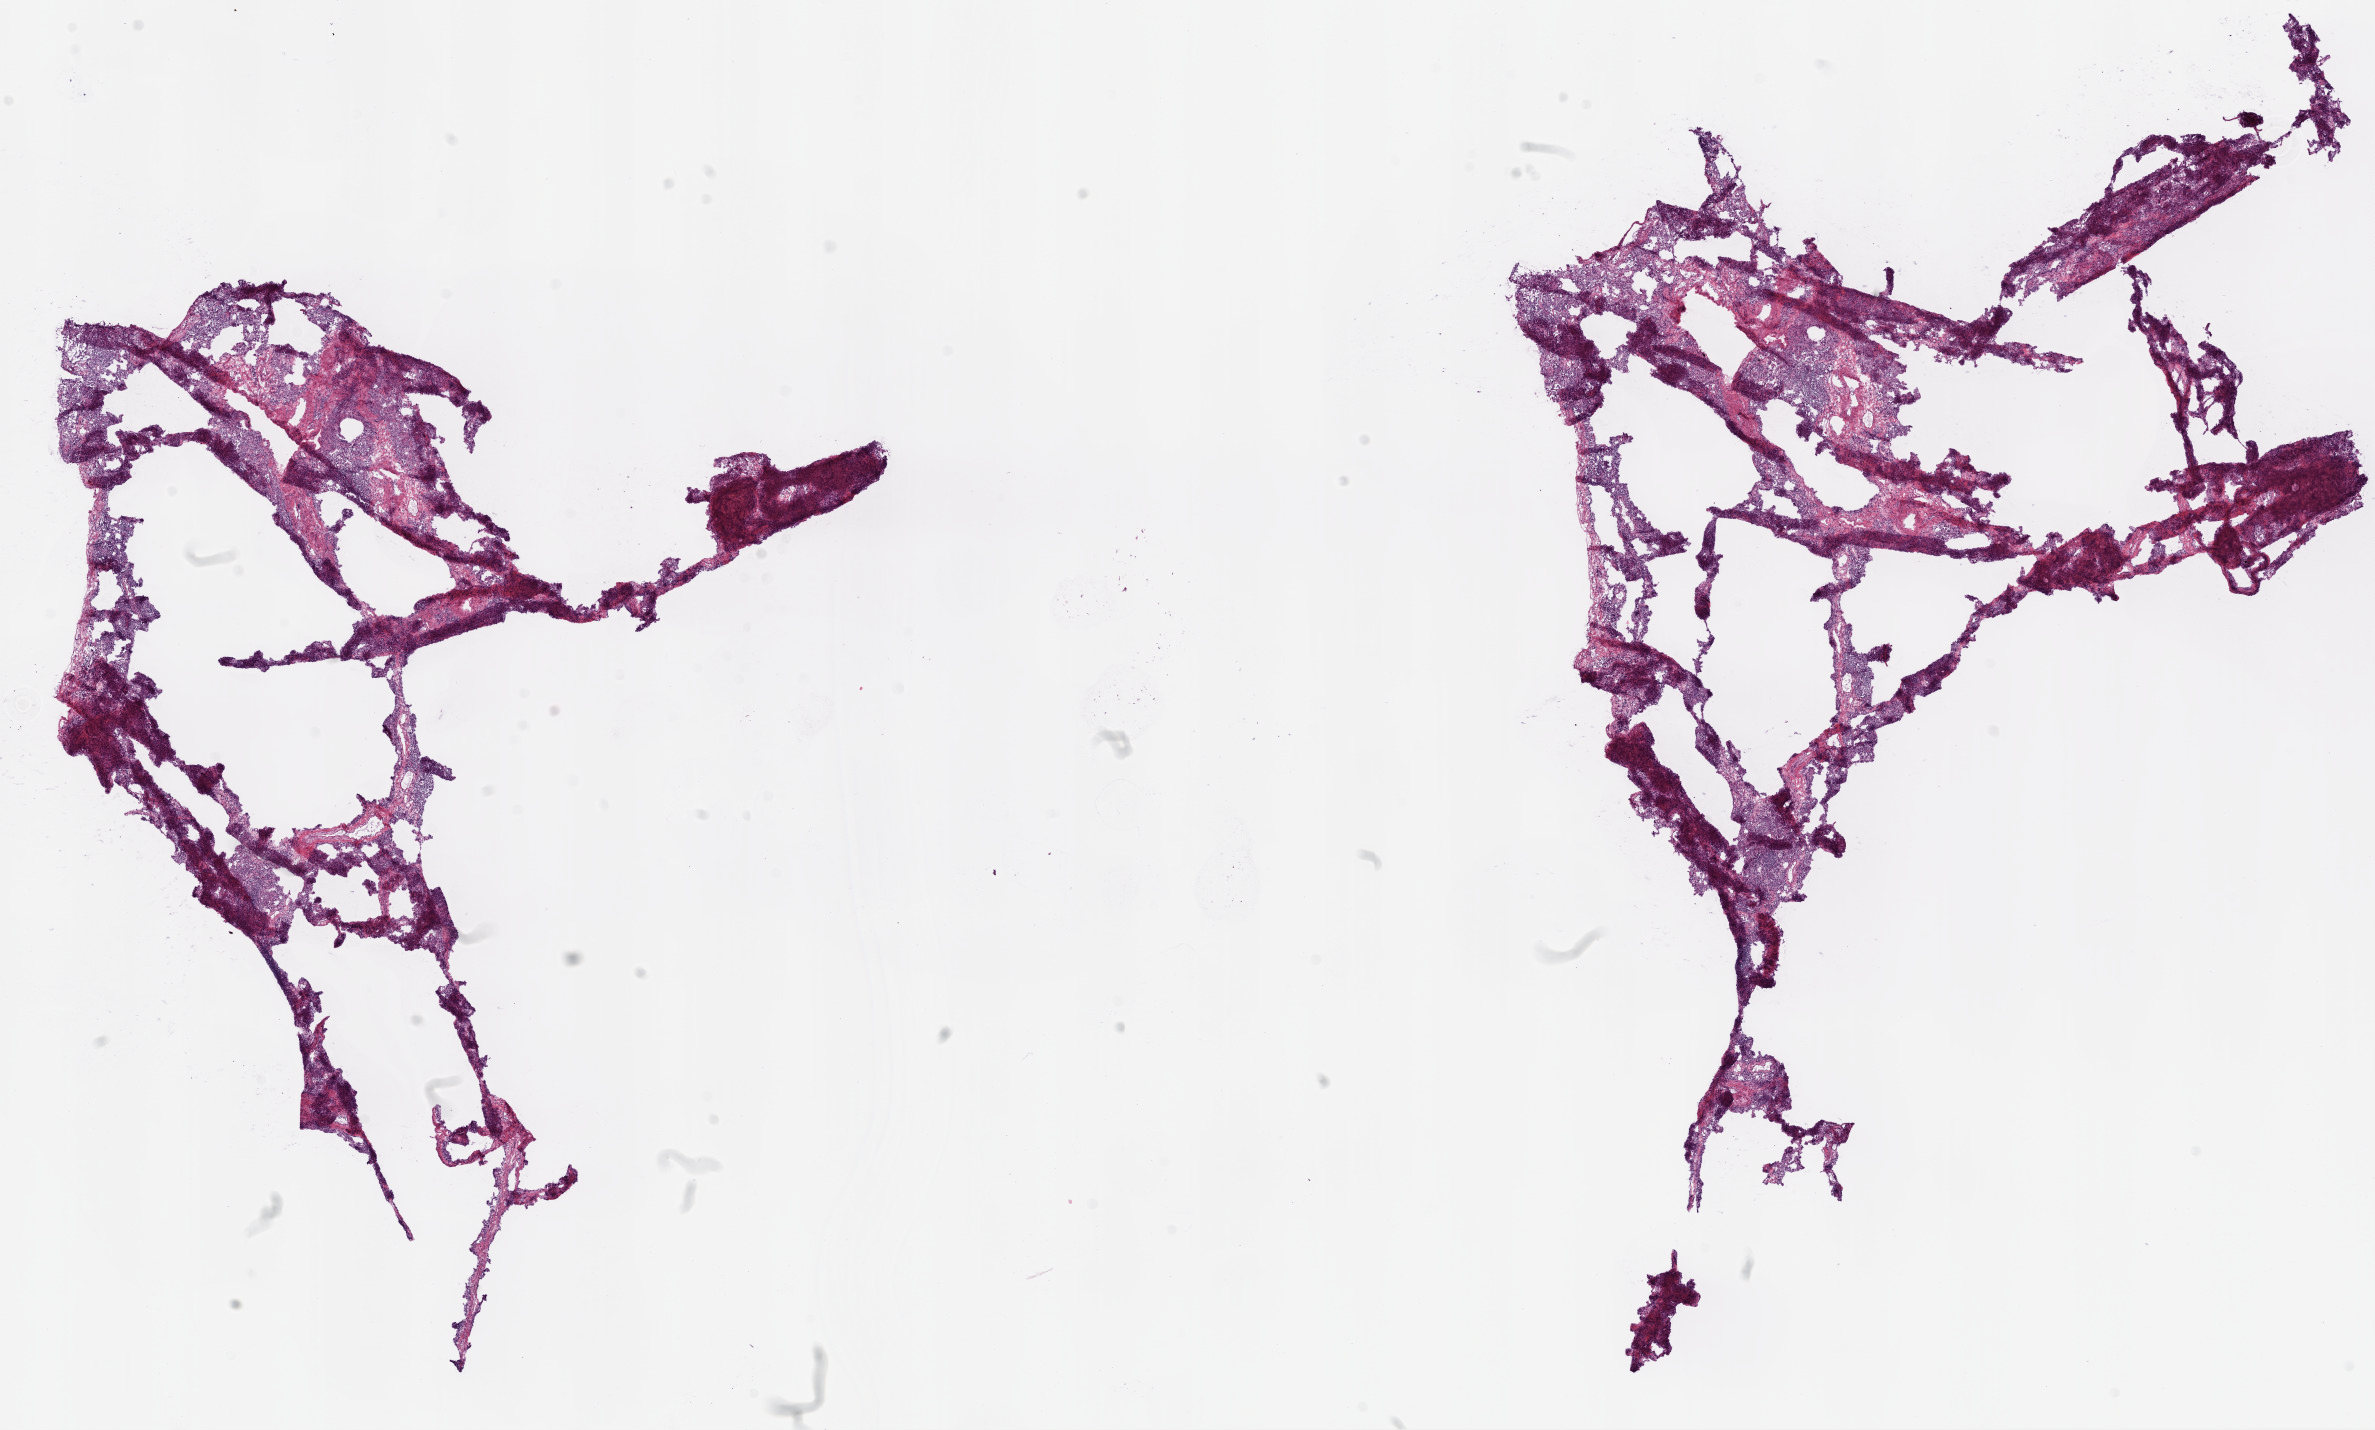
H&E-stained whole-slide image — whole scanned area (about 19.1 x 11.5 mm, slide scanned at 20x) shown as a low-resolution overview, frozen section from the top of the tissue portion, lung, solid tissue normal (non-tumour tissue) sample. Patient: male, age at initial diagnosis 64 years.
* this section: solid tissue normal (non-tumour) sample from the same patient
* patient diagnosis: Squamous cell carcinoma, NOS (upper lobe, lung)